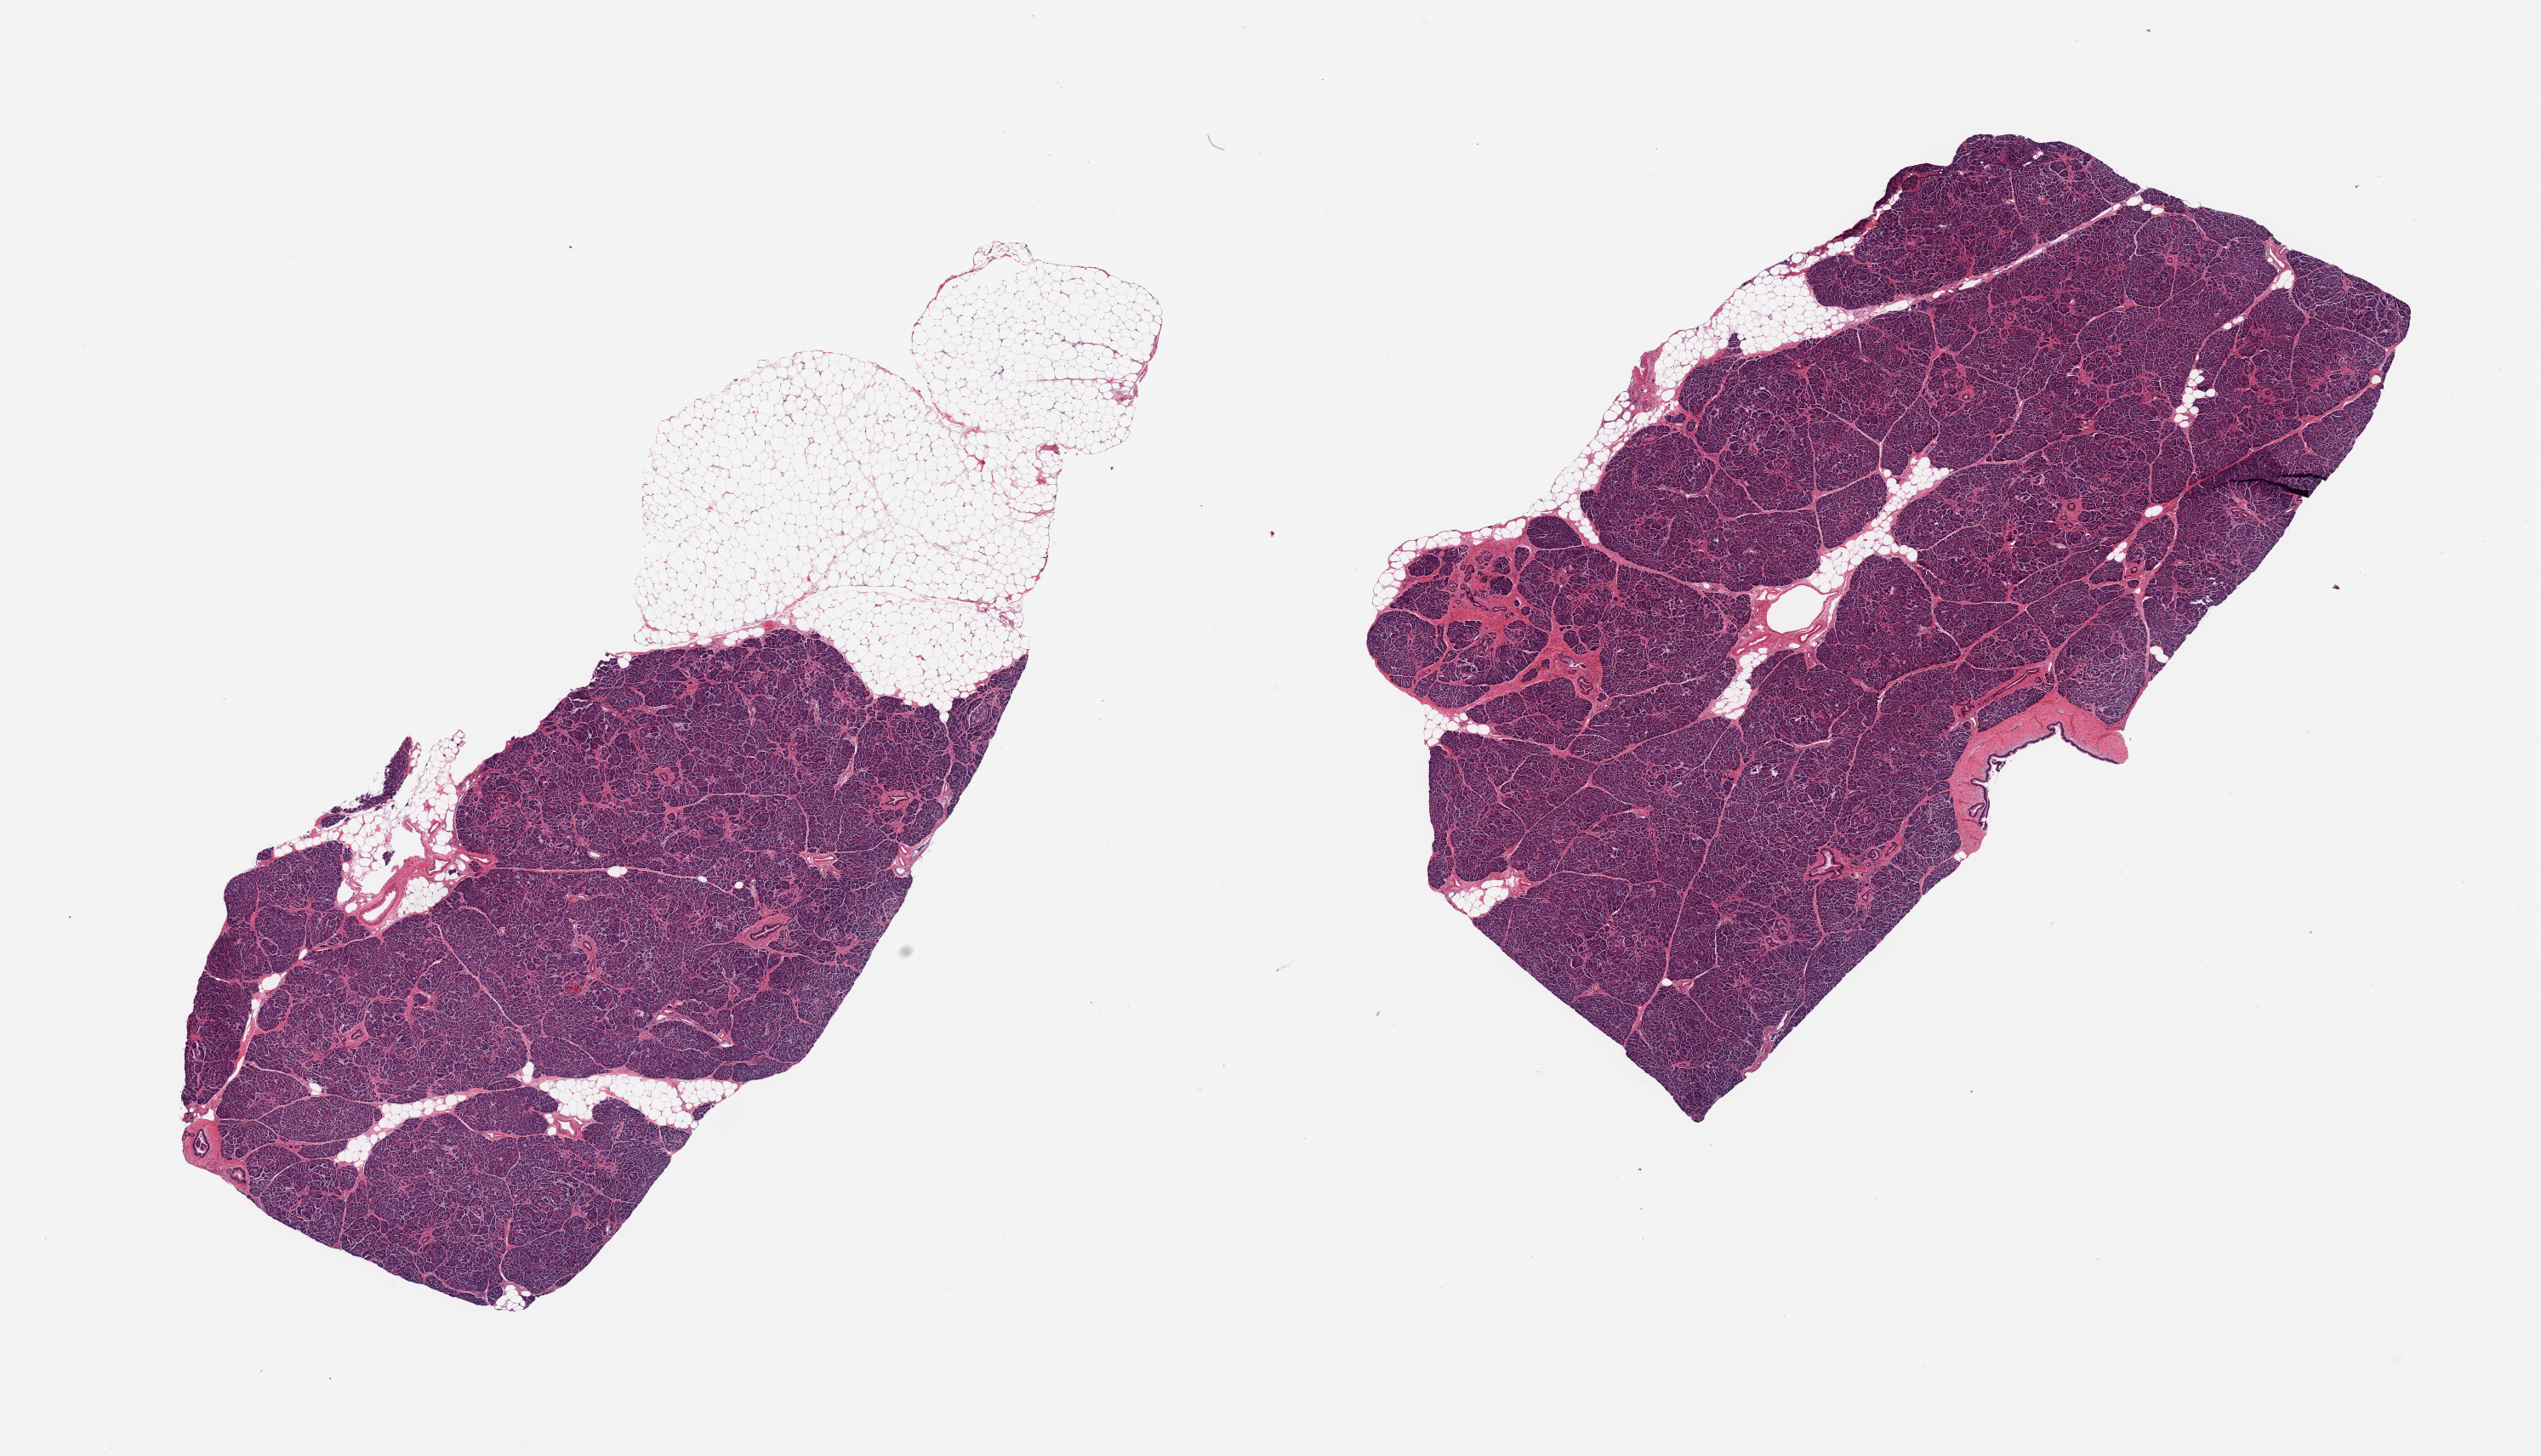
Digitized haematoxylin and eosin-stained section, low-resolution overview of the scanned area, about 23.6 x 13.5 mm; PAXgene-fixed, paraffin-embedded tissue; target tissue: pancreas; tissue donor sample. Donor: male.
Reviewer comment on this tissue sample: 2 pieces, Islets scarce but fairly well preserved, approaching score '2'.